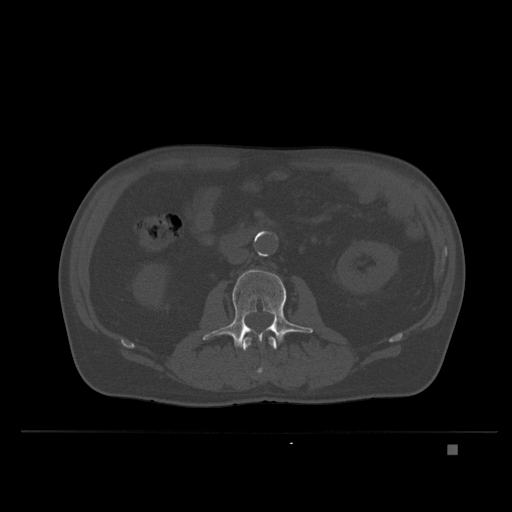
CT including the spine, one axial slice. Slice 101 of 435 in the series (ordered by position). Bone window (W 1800 / L 400 HU). 1.5 mm slice thickness. 512 × 512 image matrix, field of view 434 × 434 mm. Patient: male, 73 years. From the clinical record (not read from this slice): primary cancer: skin.
Outlined on this slice (semi-automatic segmentation, software-assisted and operator-edited):
- L2 vertebra: box from (x=243, y=336) to (x=277, y=378) px
- L3 vertebra: (x=203, y=269)–(x=313, y=349)